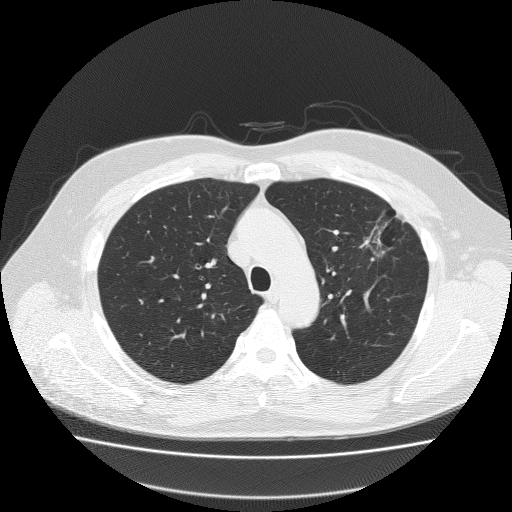
Chest CT (low-dose screening protocol), one axial image; first (baseline) screen; lung window (W 1500 / L -600 HU); 2 mm slice thickness; slice 57 of 204 in the series; 512 × 512 image matrix. Male participant, aged 62 years at enrolment. Former smoker at enrolment.
Expert-annotated lung lesion, box from (x=355, y=201) to (x=423, y=261) px. Reader record for this screening exam (exam-level; its link to the box is not recorded): non-calcified nodule or mass ≥4 mm, left upper lobe, 18 × 8 mm, spiculated (stellate) margins, soft tissue attenuation. Official screen result: positive, change unspecified: nodule(s) >= 4 mm or enlarging nodule(s), mass(es), or other non-specific abnormalities suspicious for lung cancer. Lung cancer was diagnosed 49 days after this screen: bronchiolo-alveolar adenocarcinoma, NOS, left upper lobe, well differentiated (G1), stage IA (AJCC 6th edition), 25 mm at pathology.